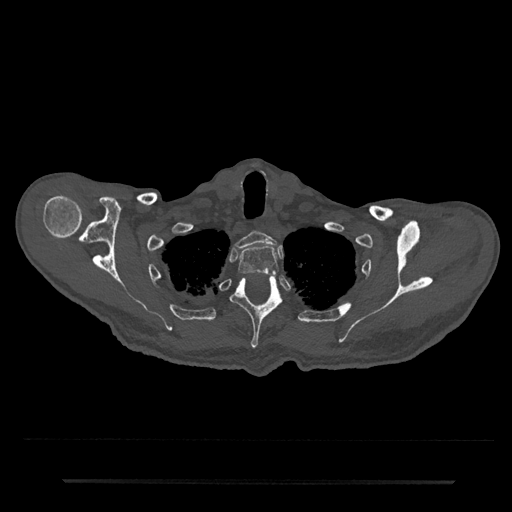
CT including the spine, one axial slice. Slice 670 of 797 in the series (ordered by position). Reconstruction kernel Br40s/3. 120 kVp. Bone window (W 1800 / L 400 HU). 0.5 mm slice thickness. 512 × 512 image matrix. Patient: male, 74 years. From the clinical record (not read from this slice): primary cancer: prostate.
Outlined on this slice (semi-automatically segmented with operator editing):
- T1 vertebra: bounding box (x1, y1, x2, y2) in pixels: (235, 231, 277, 249)
- T2 vertebra: (238, 245, 279, 275)
- T3 vertebra: (231, 275, 282, 349)